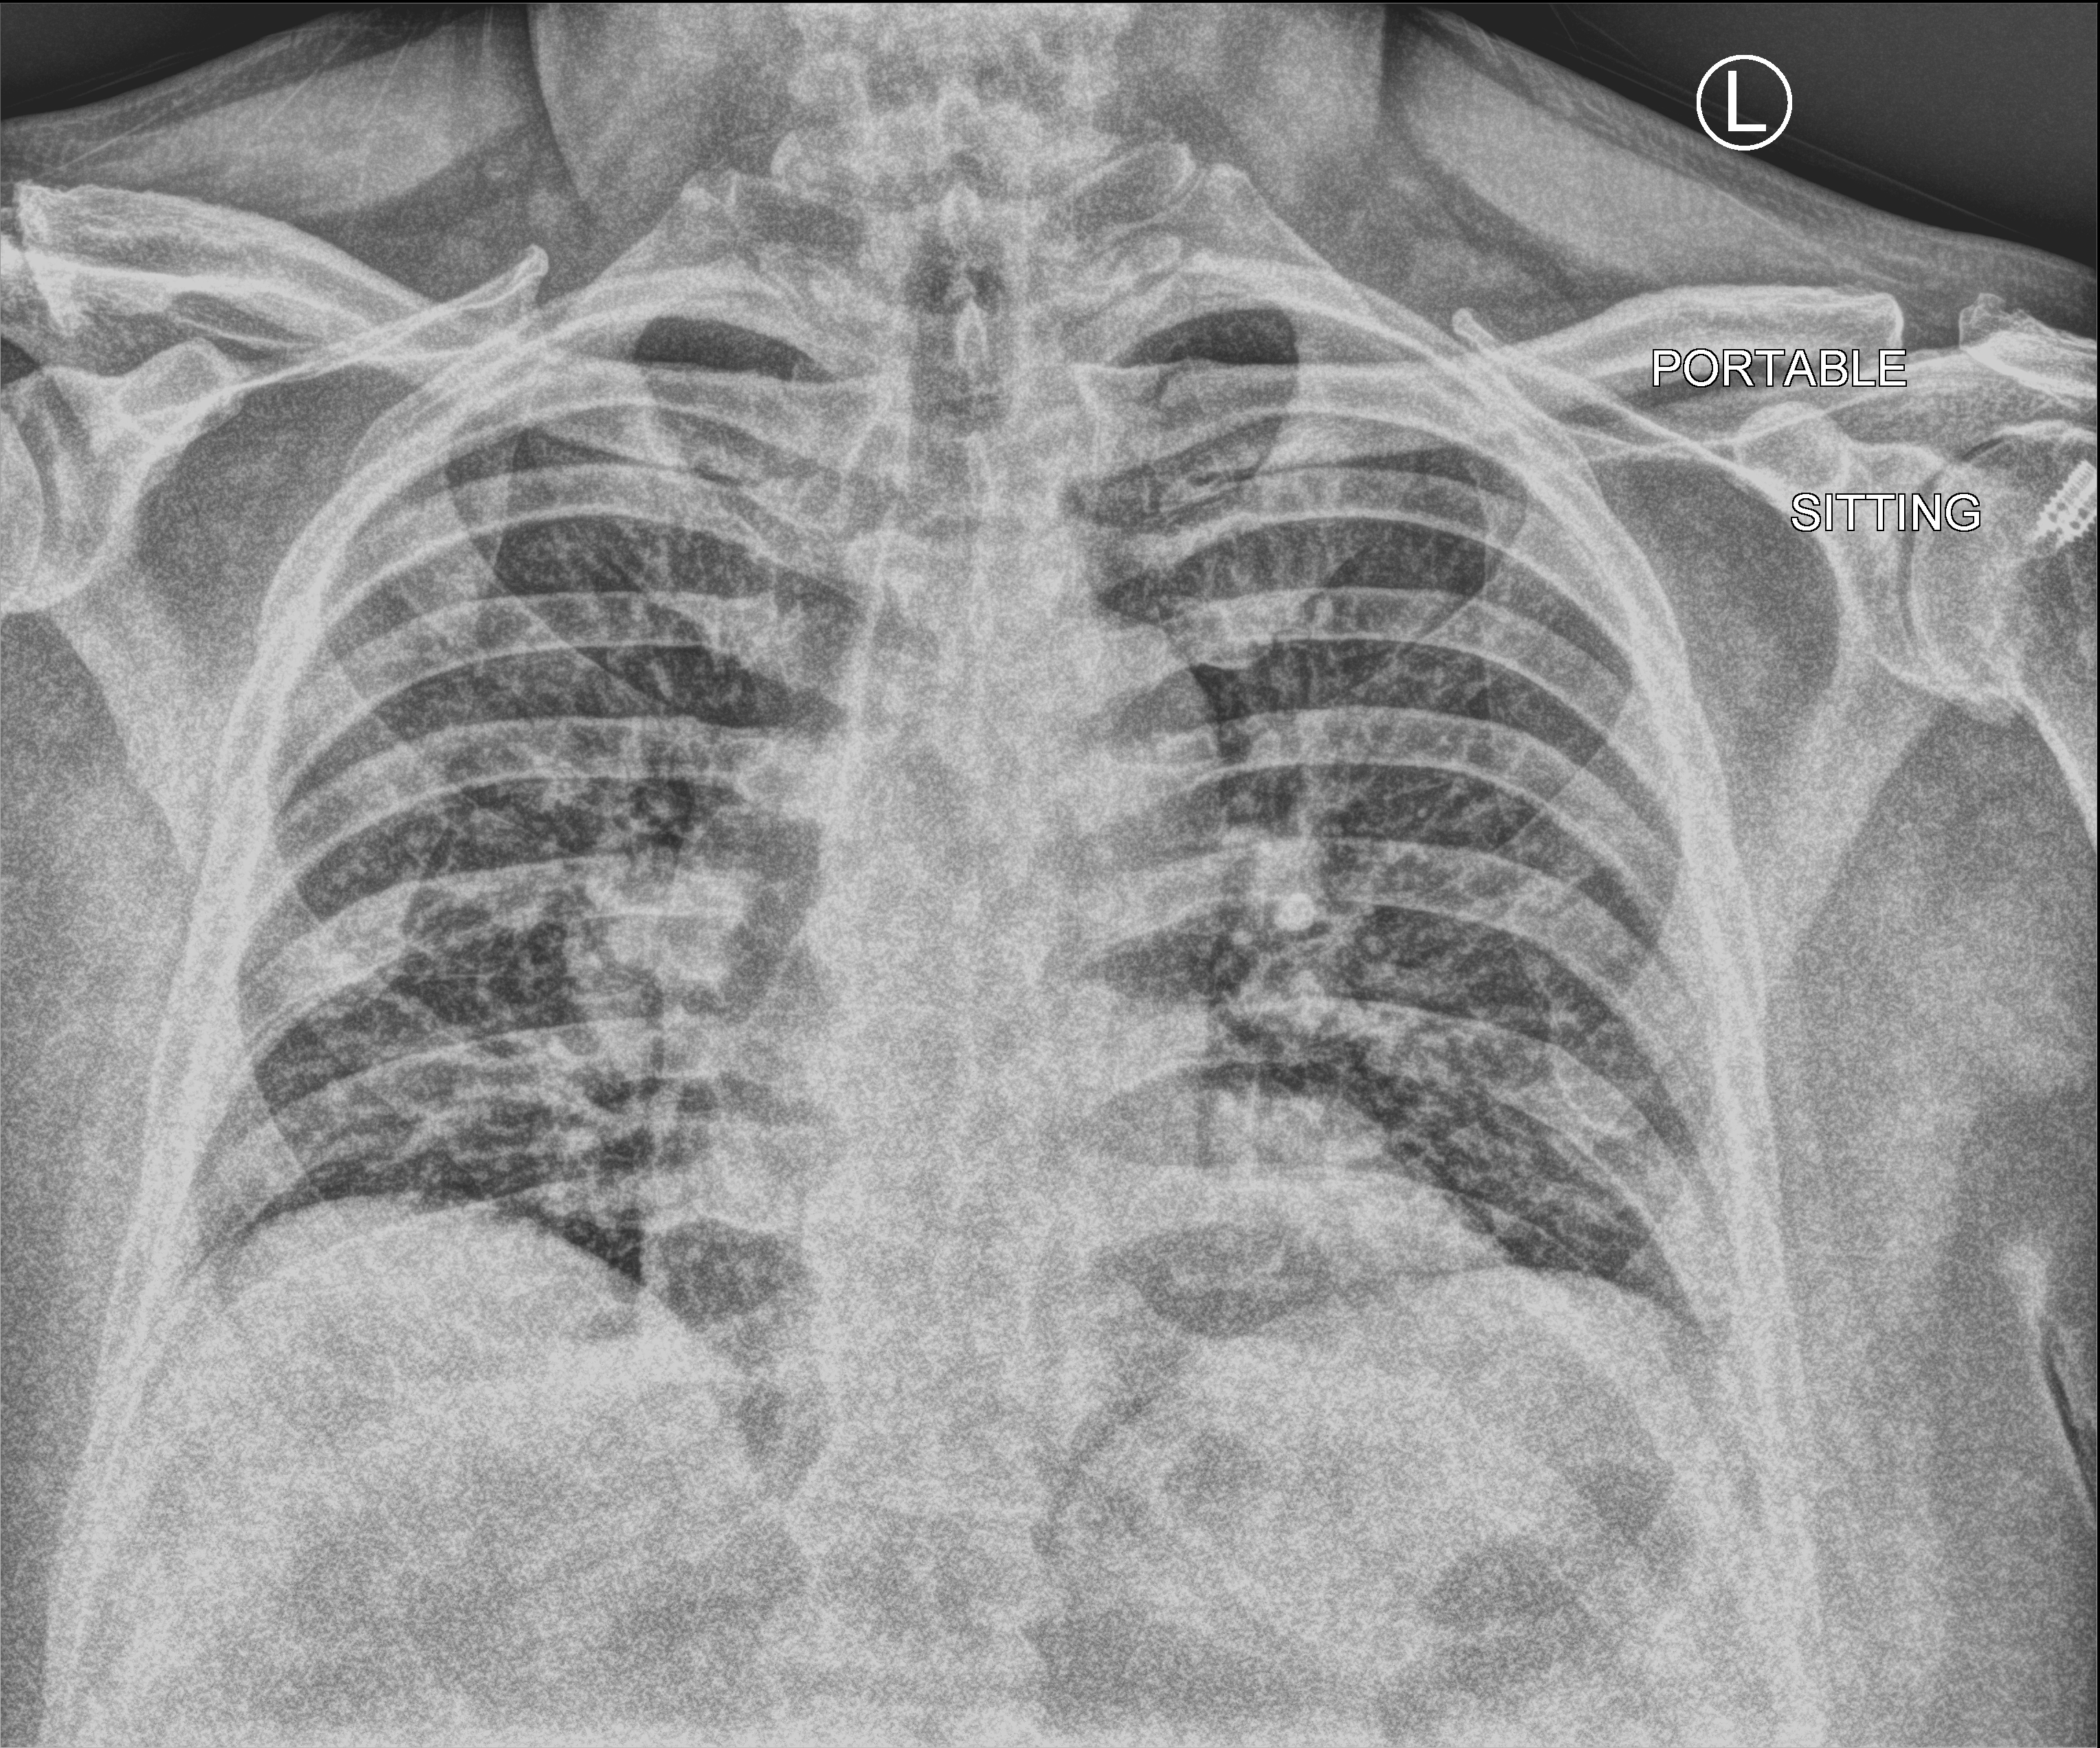
Portable chest radiograph. Male patient hospitalised with COVID-19, age 60–74 years.
Admission-level facts for this patient (not findings on this image; timing relative to this image not recorded): other chronic lung disease (admission record): no; mechanically ventilated during this hospital stay: no; admitted to intensive care during this hospital stay: no.